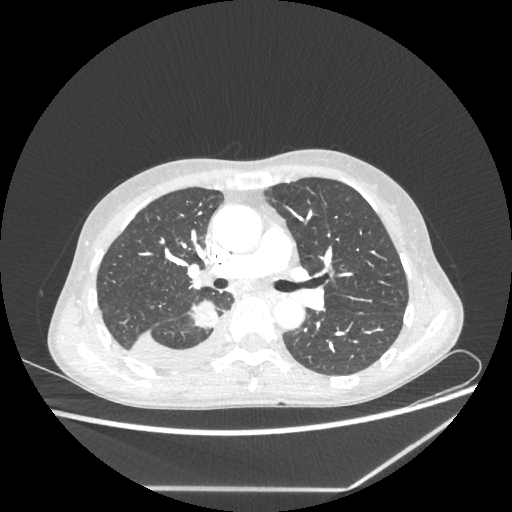
Chest CT, one axial slice. Position 139 of 237 along the scan axis. Reconstruction kernel STANDARD. 80 kVp. Lung window (W 1500 / L -600 HU). 1.25 mm slice thickness. 512 × 512 image matrix. Female patient, age 59 years. Case-level facts recorded for this patient, not image findings: clinical TNM (as recorded): T1c N1 M1.
Structures marked on this image (rectangle marked by the reading radiologist):
- lung tumour (recorded histology: adenocarcinoma): bounding box (x1, y1, x2, y2) in pixels: (191, 298, 219, 330)